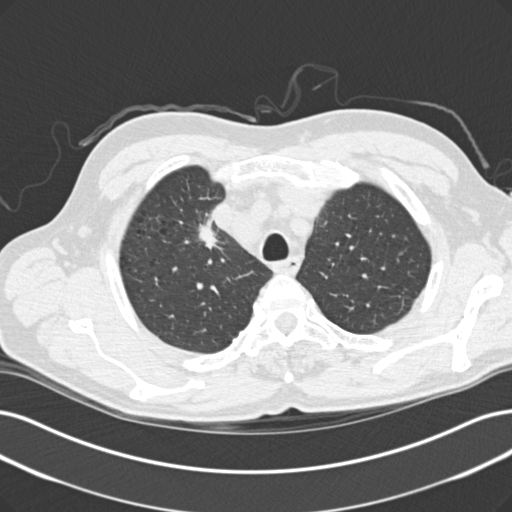
Low-dose screening chest CT, one axial slice. Position 120 of 152 along the scan axis. Lung window (W 1500 / L -600 HU). 2 mm slice thickness. 512 × 512 image matrix.
Outlined on this slice (outlined manually by an expert reader):
- lesion 1 (tumor, upper lobe of right lung): bounding box <199,219,218,249> (left, top, right, bottom; pixels)